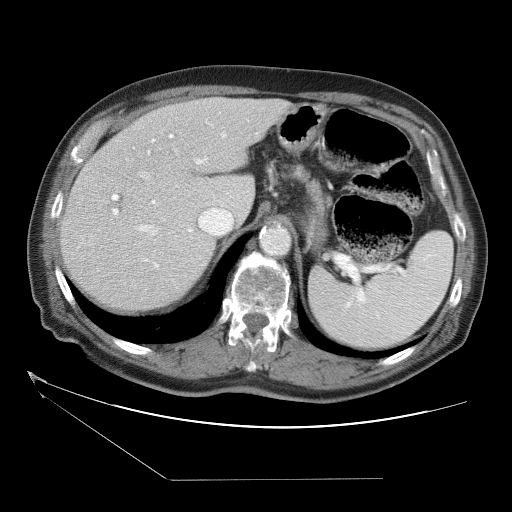
Contrast-enhanced abdominal CT (liver protocol), one axial slice; slice 24 of 38 in the series (ordered by position); reconstruction kernel STANDARD; 120 kVp; one of 2 acquisitions stored at this slice position; soft-tissue window (W 400 / L 40 HU); 5 mm slice thickness; 512 × 512 image matrix. From the clinical record (not read from this slice): diagnosis: hepatocellular carcinoma (patient treated with transarterial chemoembolisation; whether this scan precedes or follows treatment is not stated here); TNM stage (as recorded): Stage-II; Child-Pugh class: A; tumour differentiation: moderately differentiated.
Structures marked on this image (semi-automatic segmentation, software-assisted and operator-edited):
- abdominal aorta: bounding box <262,228,291,256> (left, top, right, bottom; pixels)
- liver parenchyma outside the tumour (the mass and vessels are separate outlines, so this box may not span the whole liver): <60,96,295,310>
- liver vessels: <111,132,227,269>